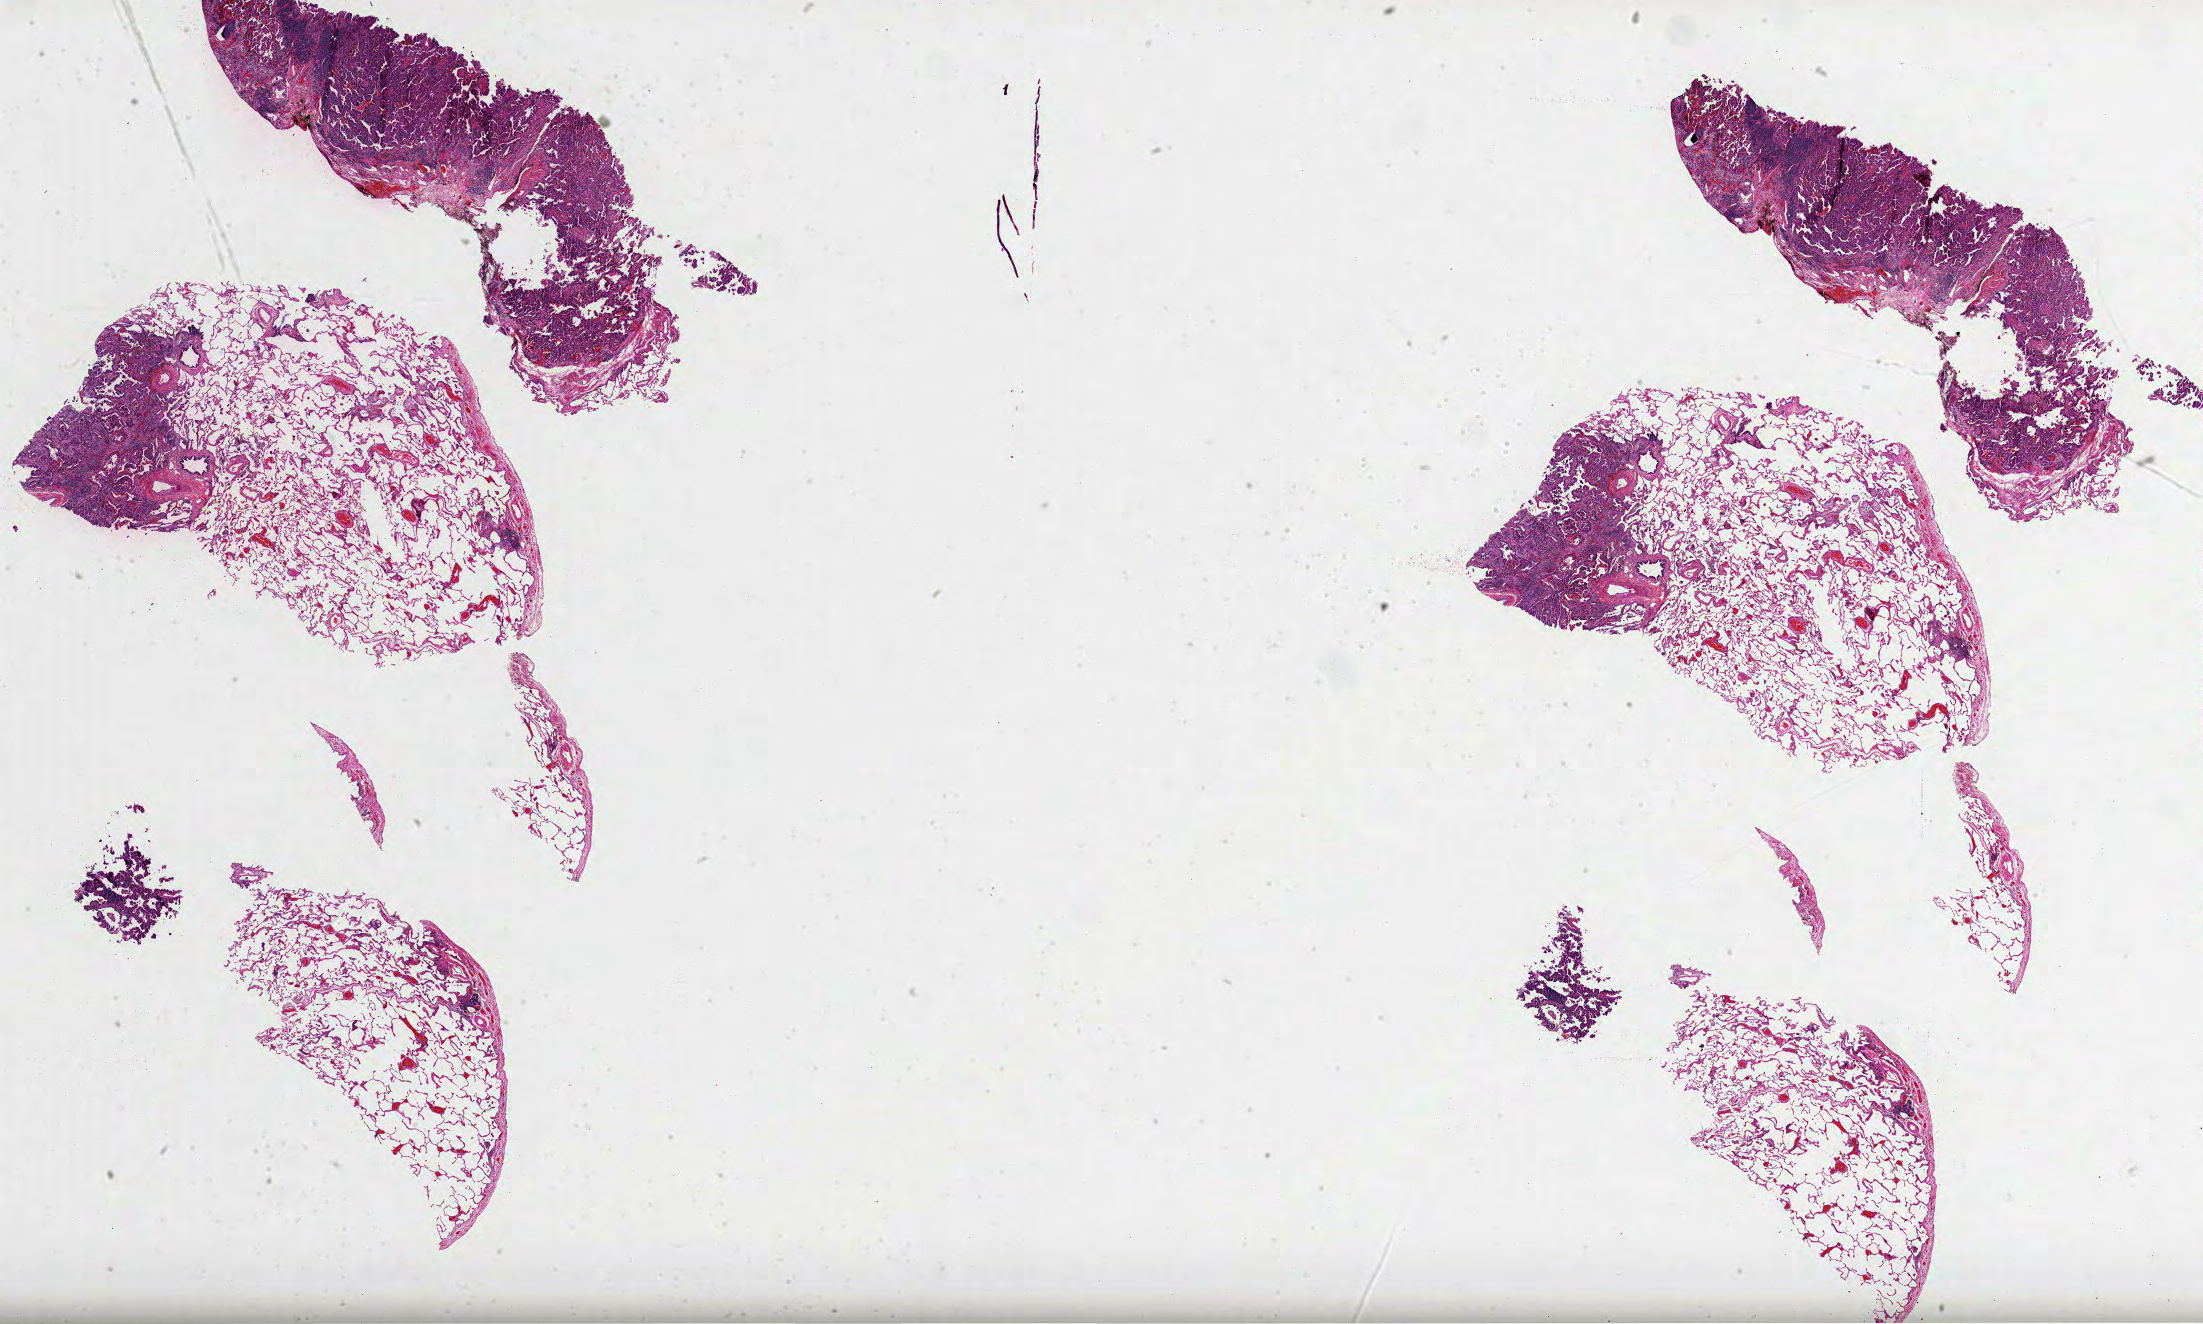
H&E-stained whole-slide image, shown as a low-resolution overview of the whole scanned area (about 35.5 x 21.4 mm, acquisition: 40x scan), FFPE section, sample: primary tumour, lung. Female patient; age at initial diagnosis 74 years.
- TNM: T1 N0 MX
- AJCC pathologic stage: IA
- histologic diagnosis: Adenocarcinoma, NOS